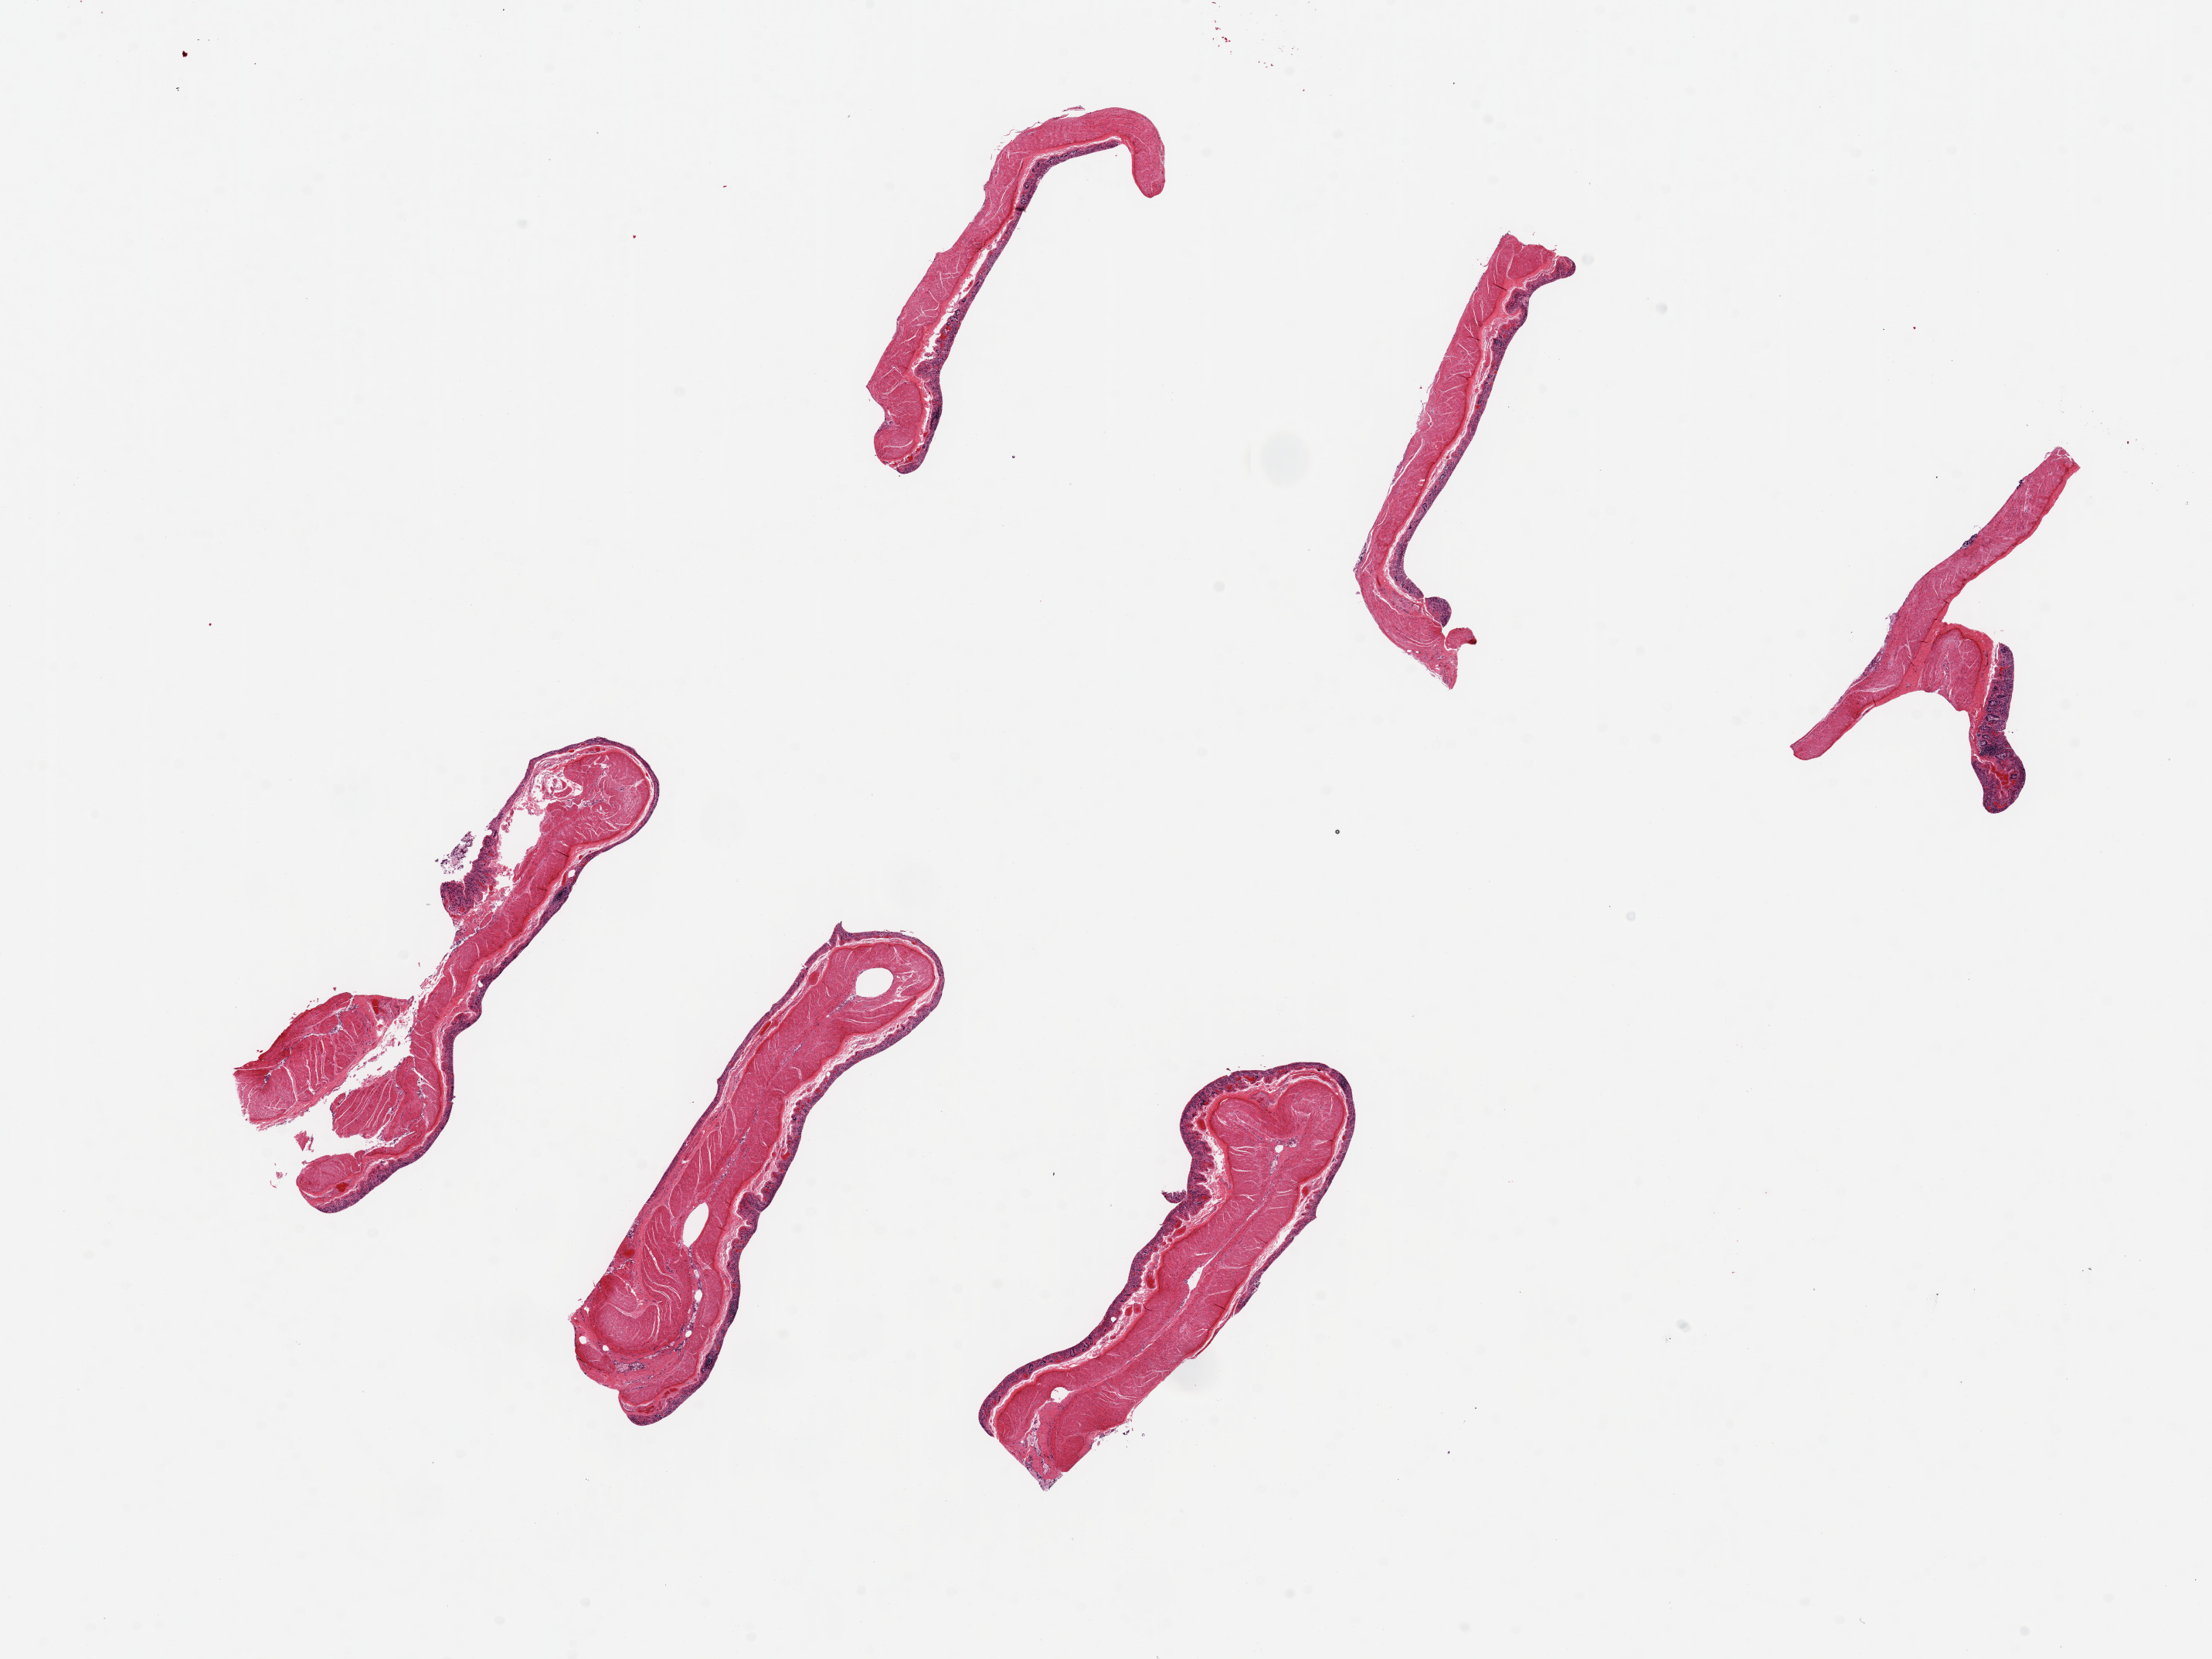
Digitized haematoxylin and eosin-stained section, shown as a low-resolution overview of the whole scanned area (about 22.6 x 17.0 mm, from a 20x scan); PAXgene-fixed, paraffin-embedded tissue; sampled site (target tissue): sigmoid colon; tissue donor sample. Donor: male.
Reviewer comment on this tissue sample: 6 pieces, up to 6x1mm; muscularis moderately autolyzed; totally autolyzed mucosa present.